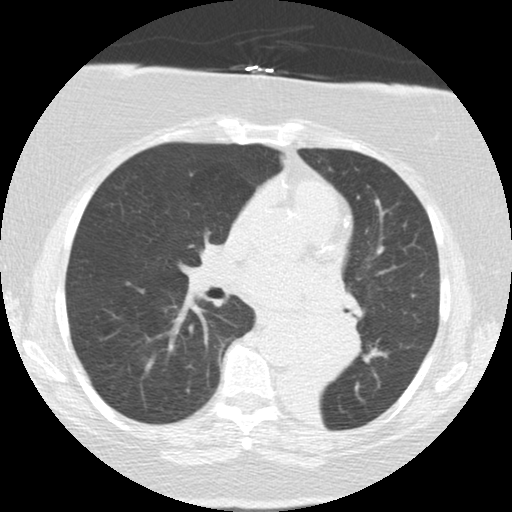
Low-dose screening chest CT, one axial slice; position 74 of 136 along the scan axis; reconstruction kernel STANDARD; 120 kVp; lung window (W 1500 / L -600 HU); 2.5 mm slice thickness; 512 × 512 image matrix, field of view 309 × 309 mm.
Structures marked on this image (manually delineated by an expert):
- lesion 2 (tumor, mediastinum): bounding box <299,311,363,382> (left, top, right, bottom; pixels)